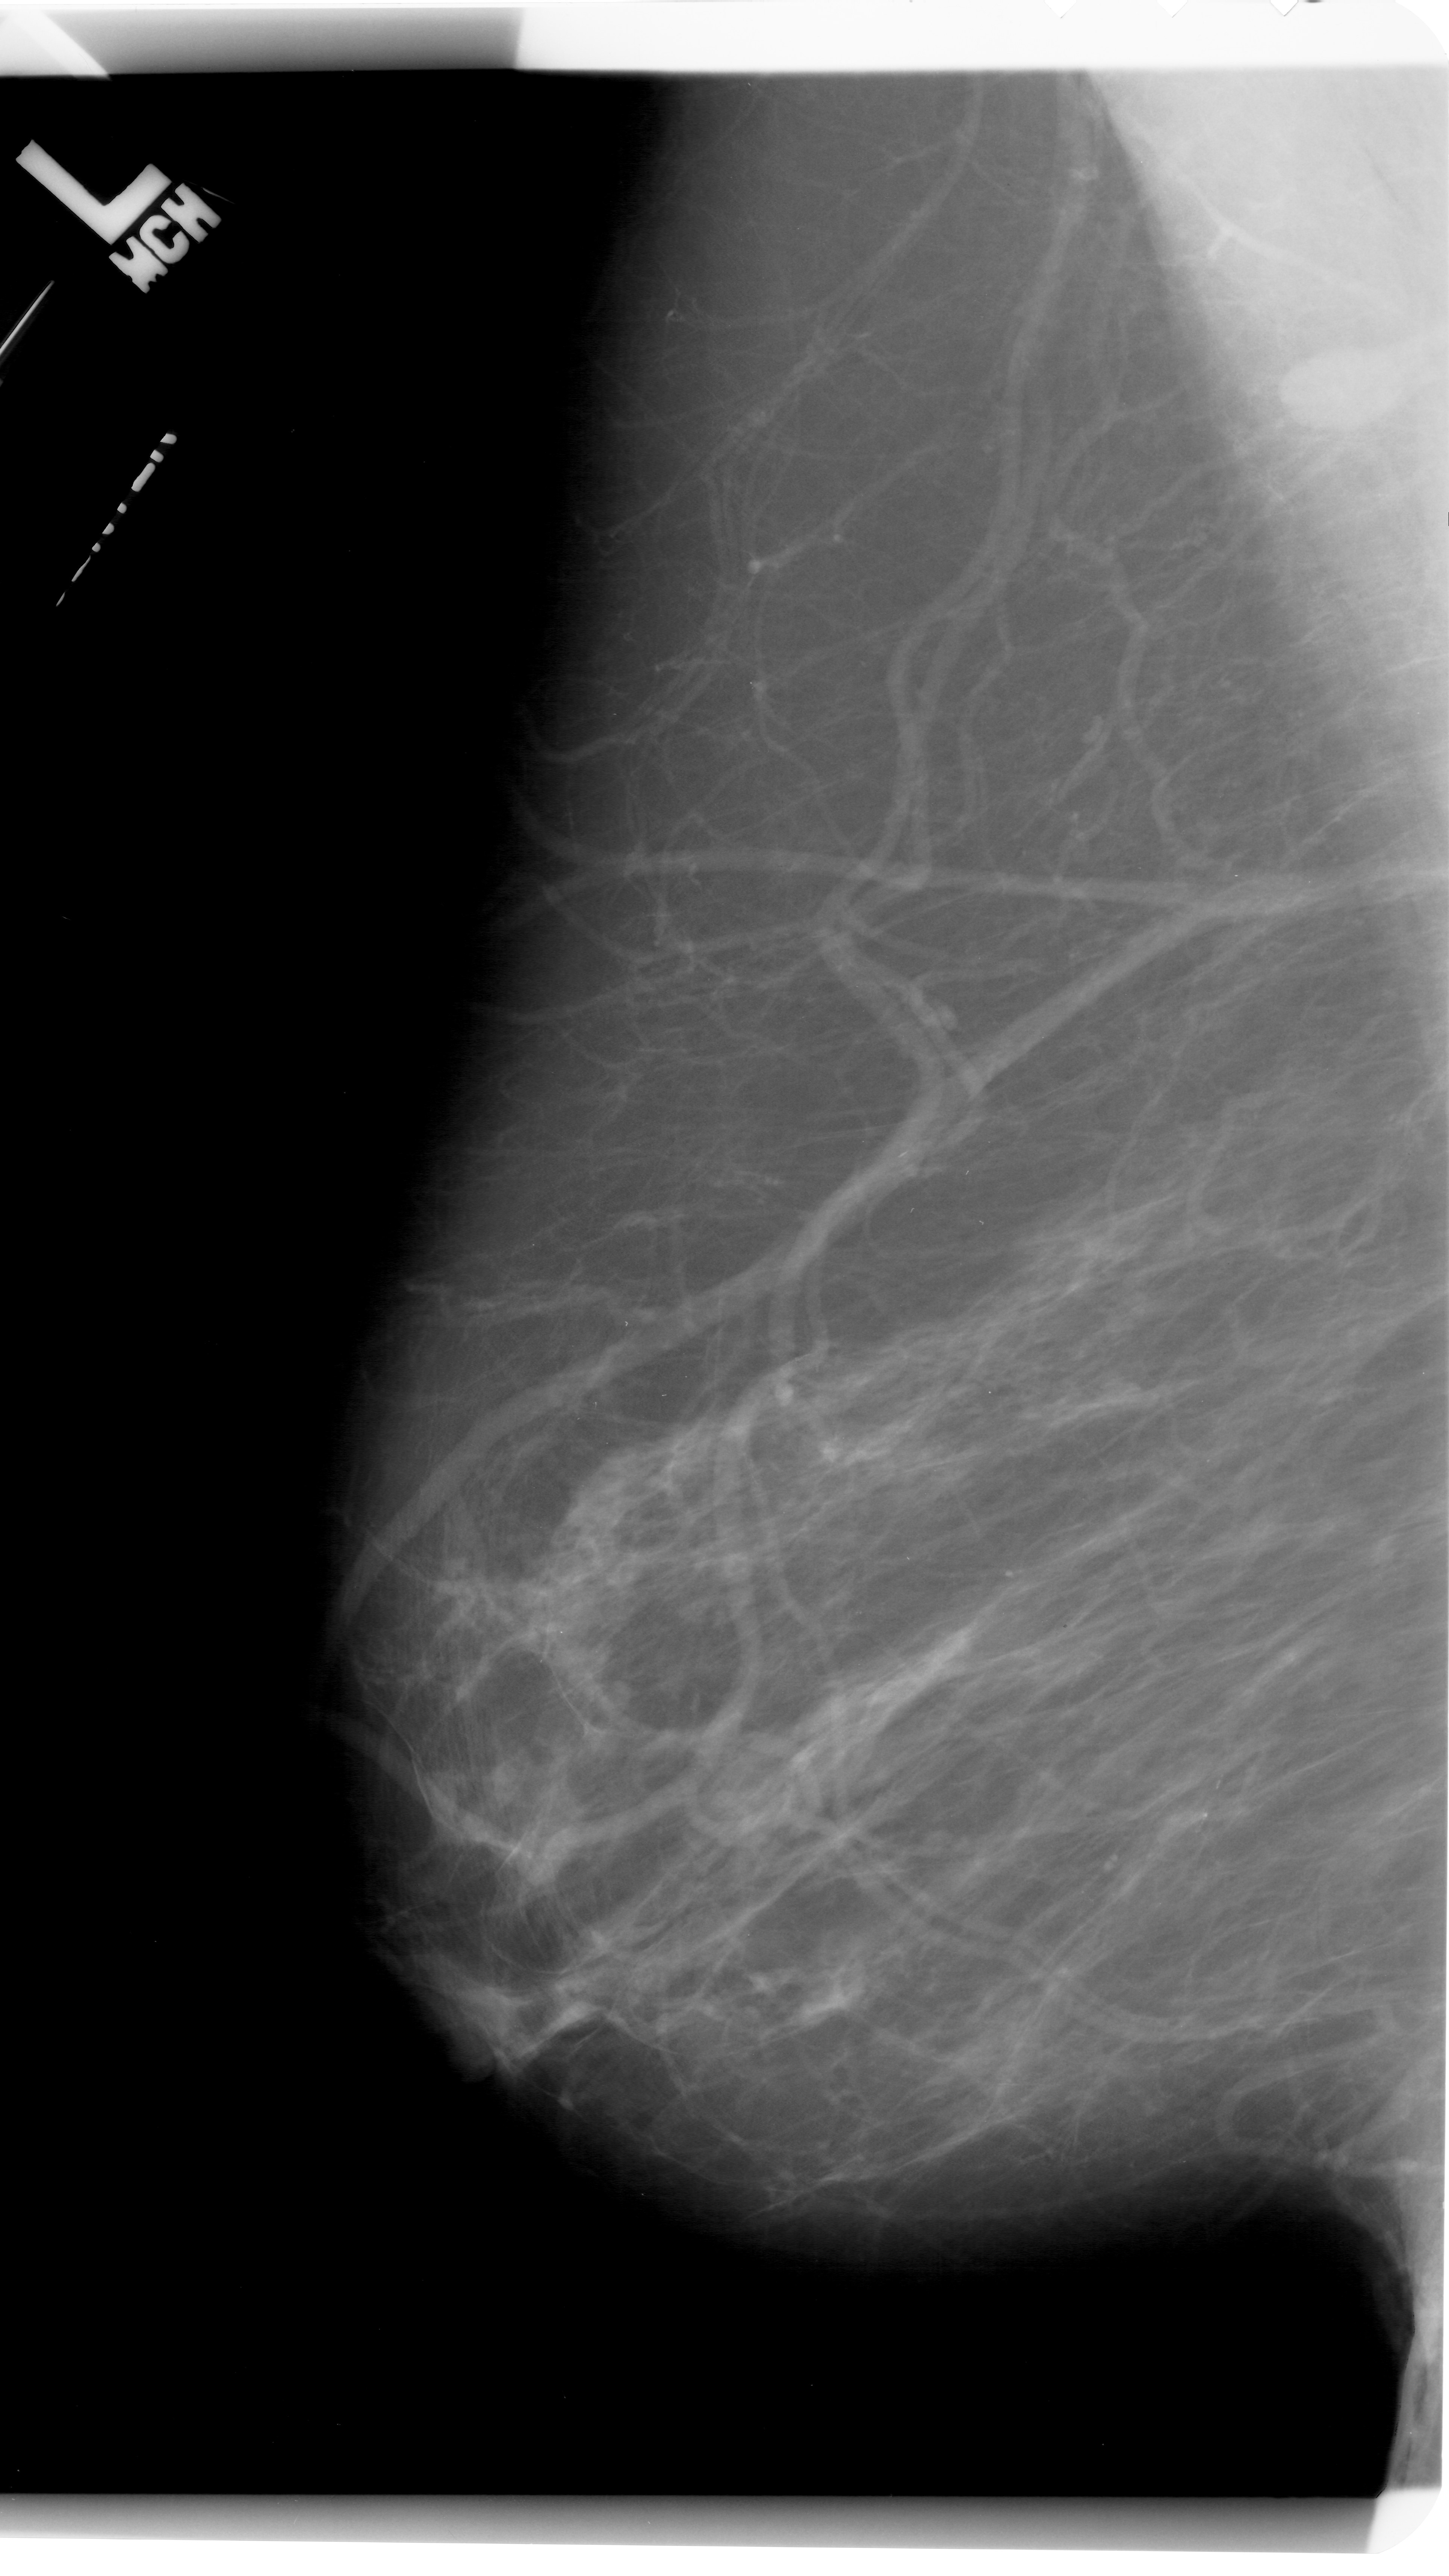
Mammogram (digitized film); left breast; MLO view; breast composition: scattered fibroglandular densities (BI-RADS density category 2 of 4); 1449 × 2576 image matrix.
Marked abnormalities (boxes around the expert regions of interest):
- calcifications, morphology fine linear branching, distribution linear; BI-RADS assessment category 4; pathology result (as recorded, not read from the image): malignant: bounding box [x1, y1, x2, y2] px = [1178, 1753, 1248, 1853]